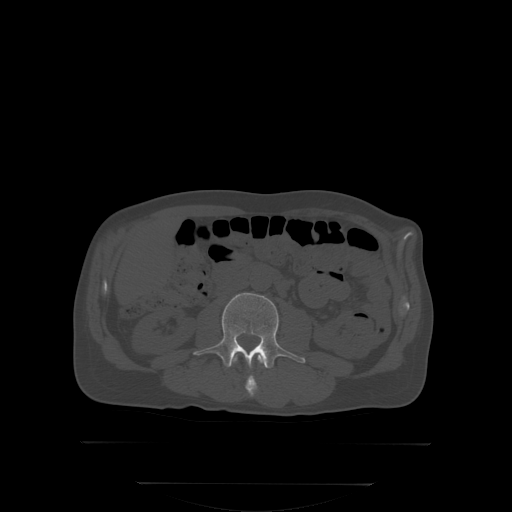
CT including the spine, one axial slice; position 126 of 350 along the scan axis; bone window (W 1800 / L 400 HU); 2.5 mm slice thickness; 512 × 512 image matrix, field of view 500 × 500 mm. Patient: male, 58 years. From the clinical record (not read from this slice): primary cancer: prostate; vertebrae with lytic lesions (as recorded): L1.
Outlined on this slice (semi-automatically segmented with operator editing):
- L2 vertebra: bounding box (x1, y1, x2, y2) in pixels: (232, 353, 266, 397)
- L3 vertebra: (193, 292, 305, 367)